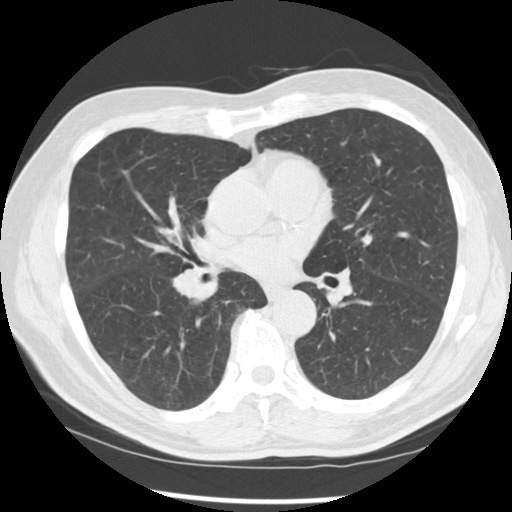
Axial slice from a low-dose chest CT screening exam, baseline screening round, lung window (W 1500 / L -600 HU), slice 144 of 277 in the series, 512 × 512 image matrix. Male participant, aged 67 years at enrolment. Current smoker at enrolment.
Expert reader's lesion annotation, bounding box [x1, y1, x2, y2] px = [157, 246, 228, 313]. The exam's reader record, not a measurement of the box and not confirmed to be the same lesion: non-calcified nodule or mass ≥4 mm, left lower lobe, 15 × 15 mm, spiculated (stellate) margins, soft tissue attenuation. Note: the box lies in the patient's right hemithorax on this image, whereas the reader's record names the left lung; they may be different findings. Participant outcome: lung cancer diagnosed 49 days after this screen — squamous cell carcinoma, NOS, right middle lobe, poorly differentiated (G3), stage IIB (AJCC 6th edition), 35 mm at pathology.